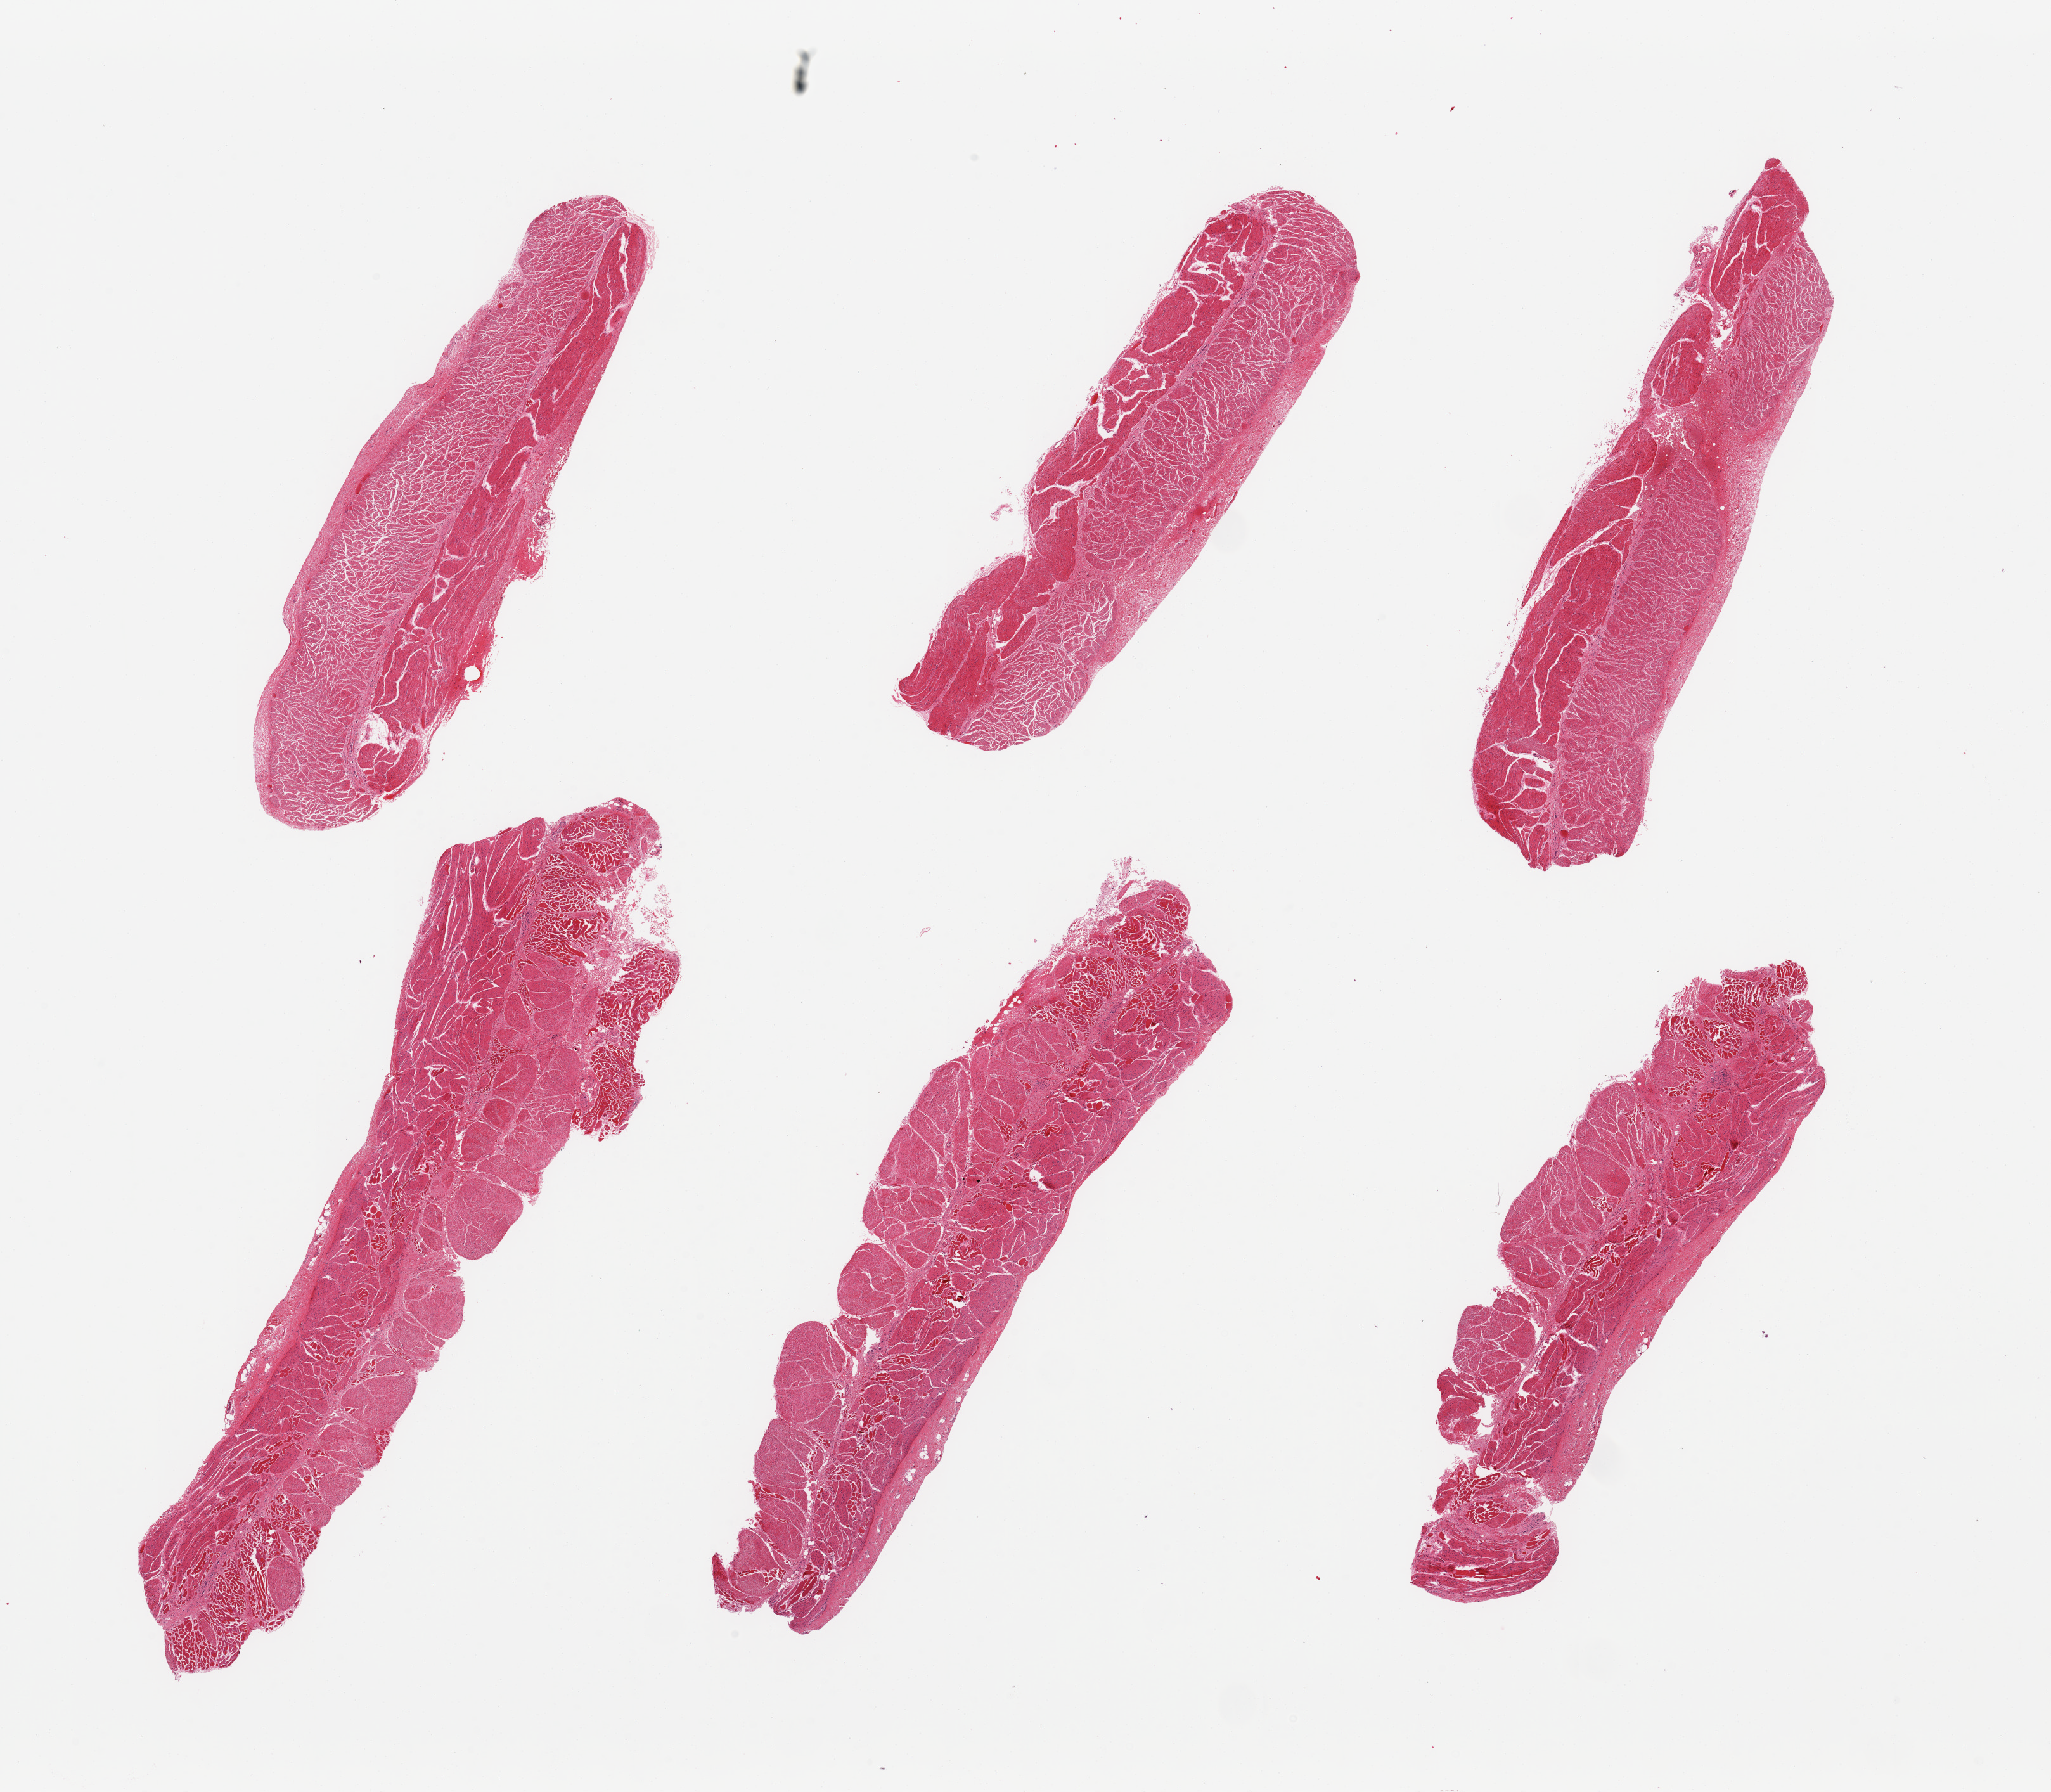
Hematoxylin and eosin (H&E) whole-slide image — a low-resolution overview of the entire scanned area, about 25.6 x 22.4 mm. PAXgene-fixed paraffin-embedded (PFPE) section. Section of esophageal muscle (target tissue). Donor tissue sample.
Reviewer comment on this tissue sample: 6 pieces; 3 pieces have up to 40% skeletal muscle admixed.